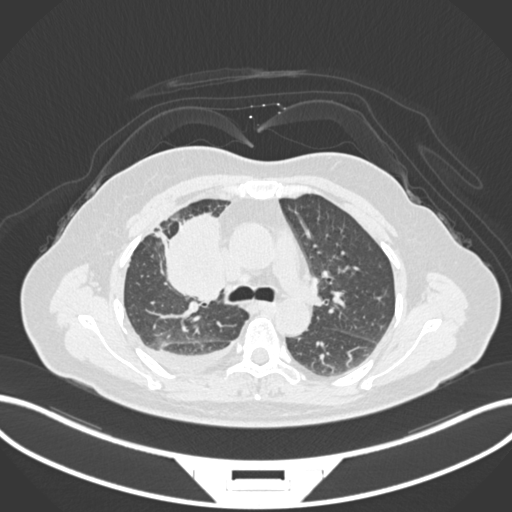
Chest CT, one axial slice. Slice 98 of 172 in the series (ordered by position). Reconstruction kernel B30f. Lung window (W 1500 / L -600 HU). 1 mm slice thickness. 512 × 512 image matrix, field of view 400 × 400 mm. Female patient, age 52 years. Case-level facts recorded for this patient, not image findings: clinical TNM (as recorded): T3 N1 M1.
Structures marked on this image (bounding box drawn by a radiologist):
- lung tumour (recorded histology: adenocarcinoma): bounding box [x1, y1, x2, y2] px = [153, 210, 225, 307]